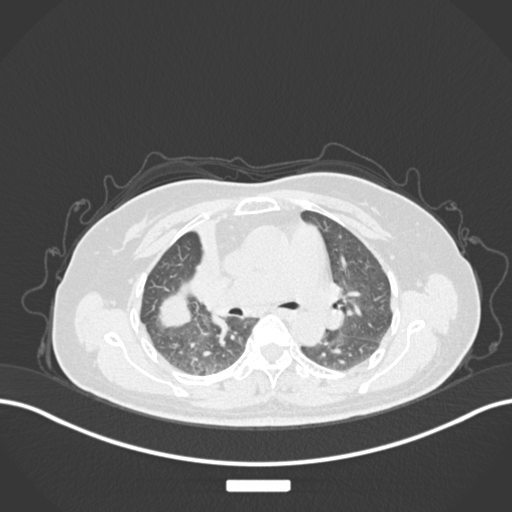
Chest CT, one axial slice; slice 92 of 177 in the series (ordered by position); reconstruction kernel B30f; lung window (W 1500 / L -600 HU); 512 × 512 image matrix, field of view 400 × 400 mm. Female patient, age 60 years. Case-level facts recorded for this patient, not image findings: clinical TNM (as recorded): T3 N1 M1.
Structures marked on this image (bounding box drawn by a radiologist):
- lung tumour (recorded histology: adenocarcinoma): box from (x=148, y=289) to (x=199, y=334) px